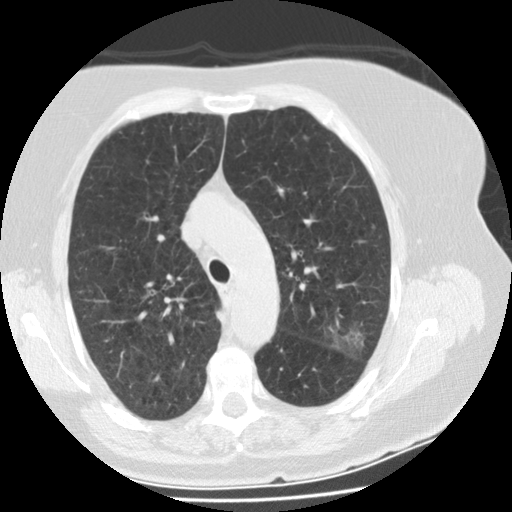
Low-dose screening chest CT, one axial slice. Position 111 of 151 along the scan axis. Reconstruction kernel STANDARD. 120 kVp. One of 2 acquisitions stored at this slice position. Lung window (W 1500 / L -600 HU). 512 × 512 image matrix.
Structures marked on this image (expert manual segmentation):
- lesion 1 (tumor, upper lobe of left lung): bounding box (x1, y1, x2, y2) in pixels: (326, 325, 365, 356)